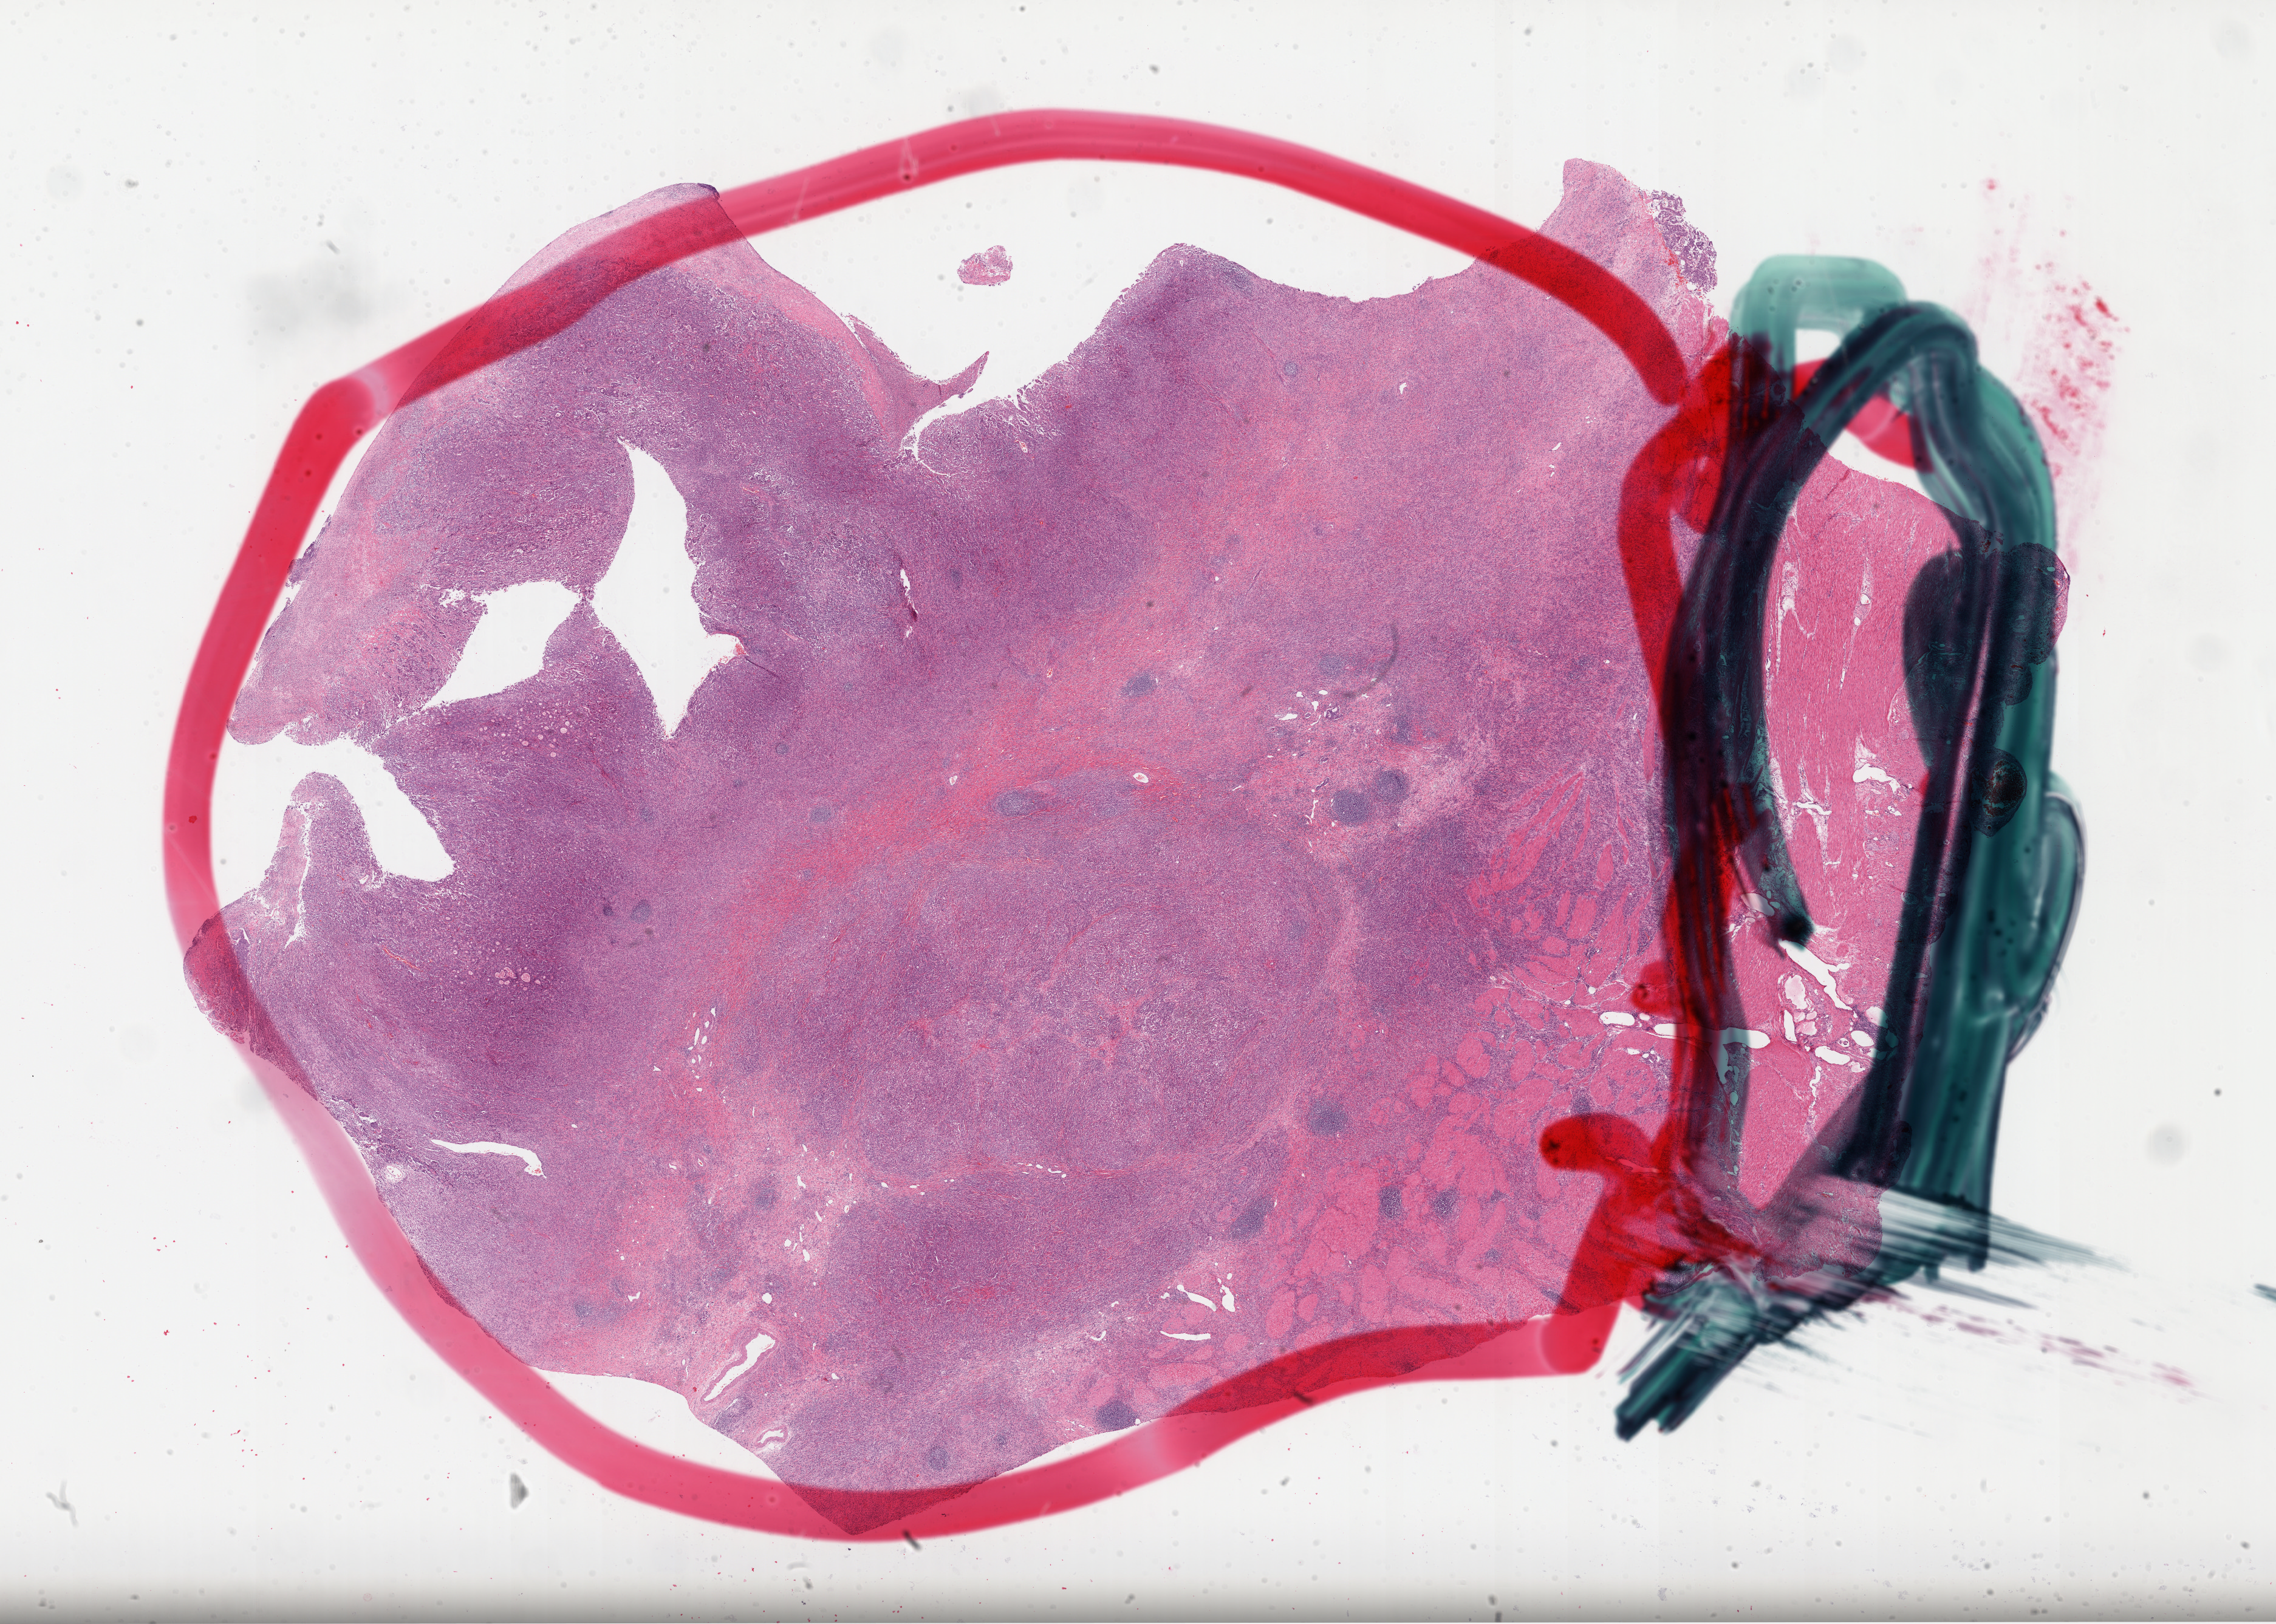
Whole-slide histology image, H&E — shown as a low-resolution overview of the whole scanned area (about 30.2 x 21.6 mm, acquisition: 40x scan), formalin-fixed paraffin-embedded (FFPE) diagnostic section, stomach, primary tumour sample. Patient: female, age at initial diagnosis 72 years. Histologic grade: G3 (poorly differentiated).
* diagnosis: Adenocarcinoma, intestinal type (gastric antrum)
* AJCC pathologic stage: IIIC